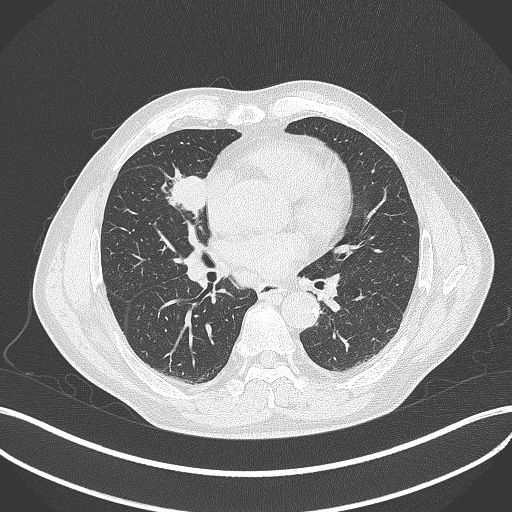
Chest CT, one axial slice. Slice 196 of 429 in the series (ordered by position). Reconstruction kernel B70f. Lung window (W 1500 / L -600 HU). 512 × 512 image matrix, field of view 400 × 400 mm. Male patient, age 61 years. Case-level facts recorded for this patient, not image findings: clinical TNM (as recorded): T2b N1 M0.
Annotated regions visible in this slice (rectangle marked by the reading radiologist):
- lung tumour (recorded histology: squamous cell carcinoma): box from (x=165, y=166) to (x=208, y=219) px